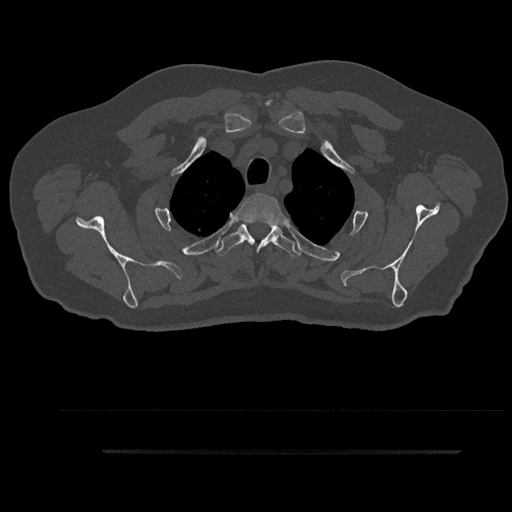
CT including the spine, one axial slice; position 735 of 797 along the scan axis; reconstruction kernel Br40s/3; bone window (W 1800 / L 400 HU); 0.5 mm slice thickness; 512 × 512 image matrix, field of view 432 × 432 mm. Male patient, age 63 years. Case-level facts recorded for this patient, not image findings: primary cancer: renal; vertebrae with lytic lesions (as recorded): T8.
Outlined on this slice (semi-automatically segmented with operator editing):
- T2 vertebra: bounding box <237,193,285,241> (left, top, right, bottom; pixels)
- T3 vertebra: <215,222,302,258>